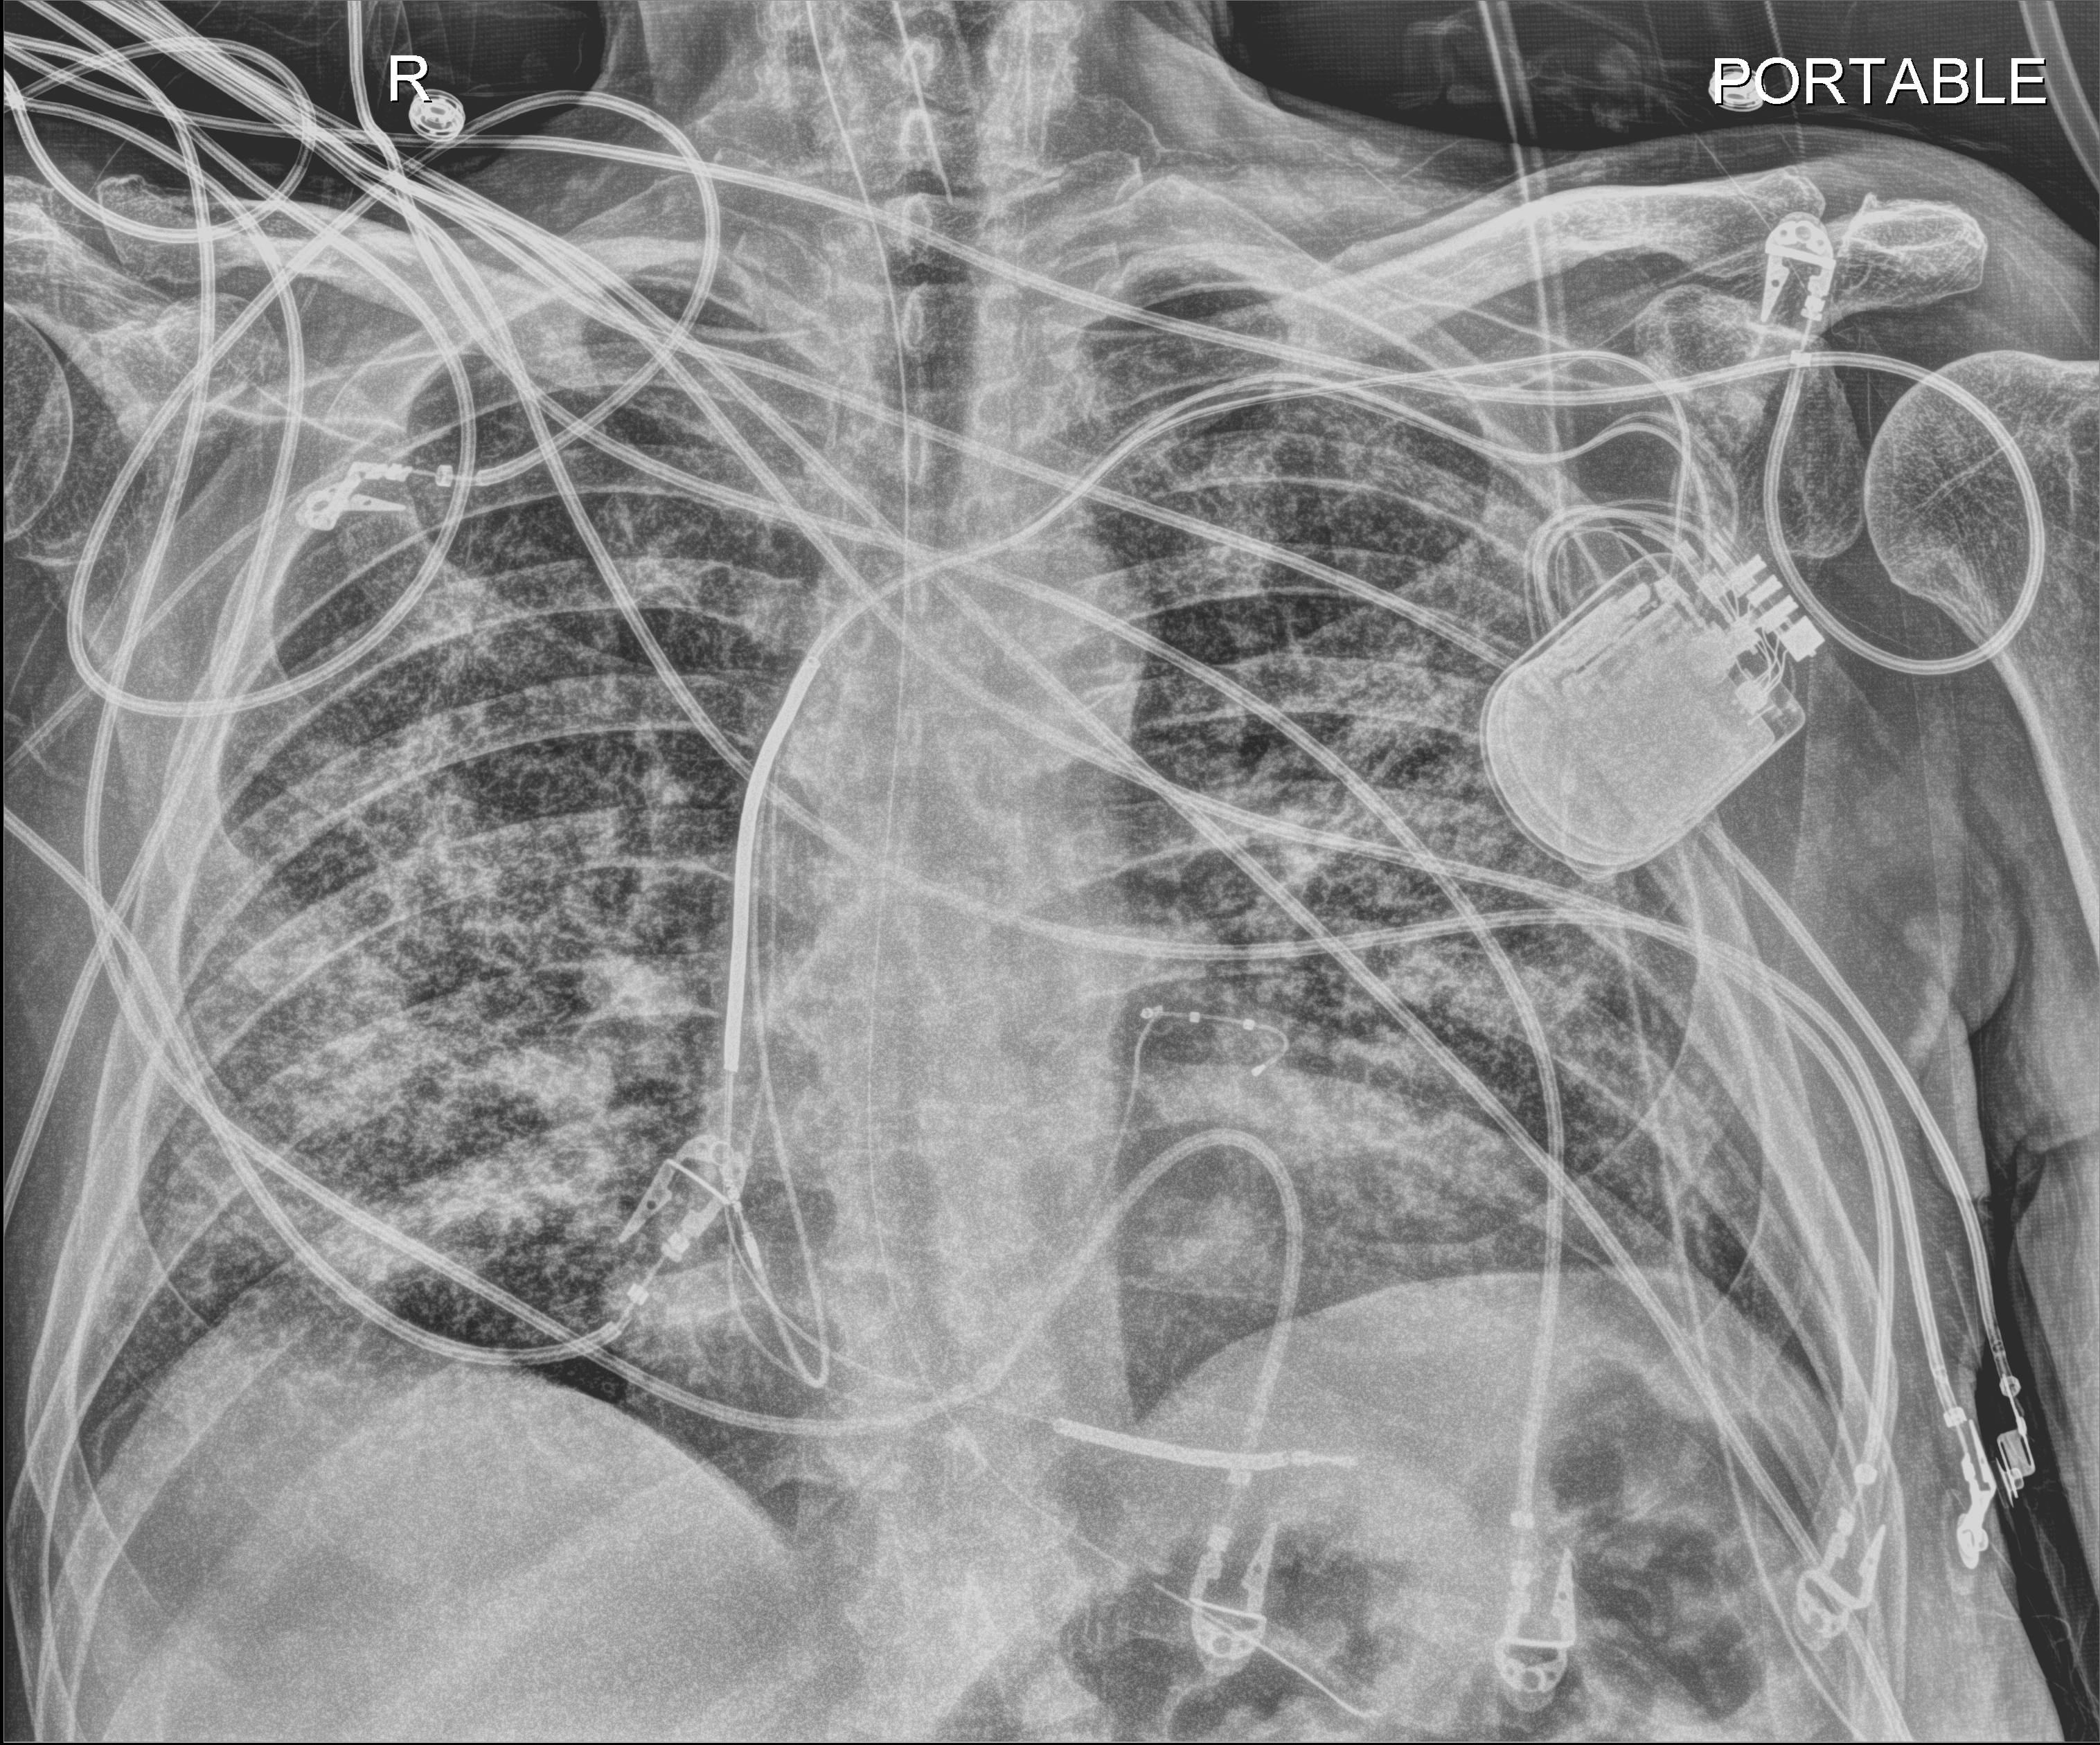
Chest X-ray (portable); anteroposterior (AP) projection. Patient hospitalised with COVID-19; male, aged 60–74 years.
Hospital-stay facts (about this admission, not read from this image; timing relative to this image not recorded): length of hospital stay: 36 days.